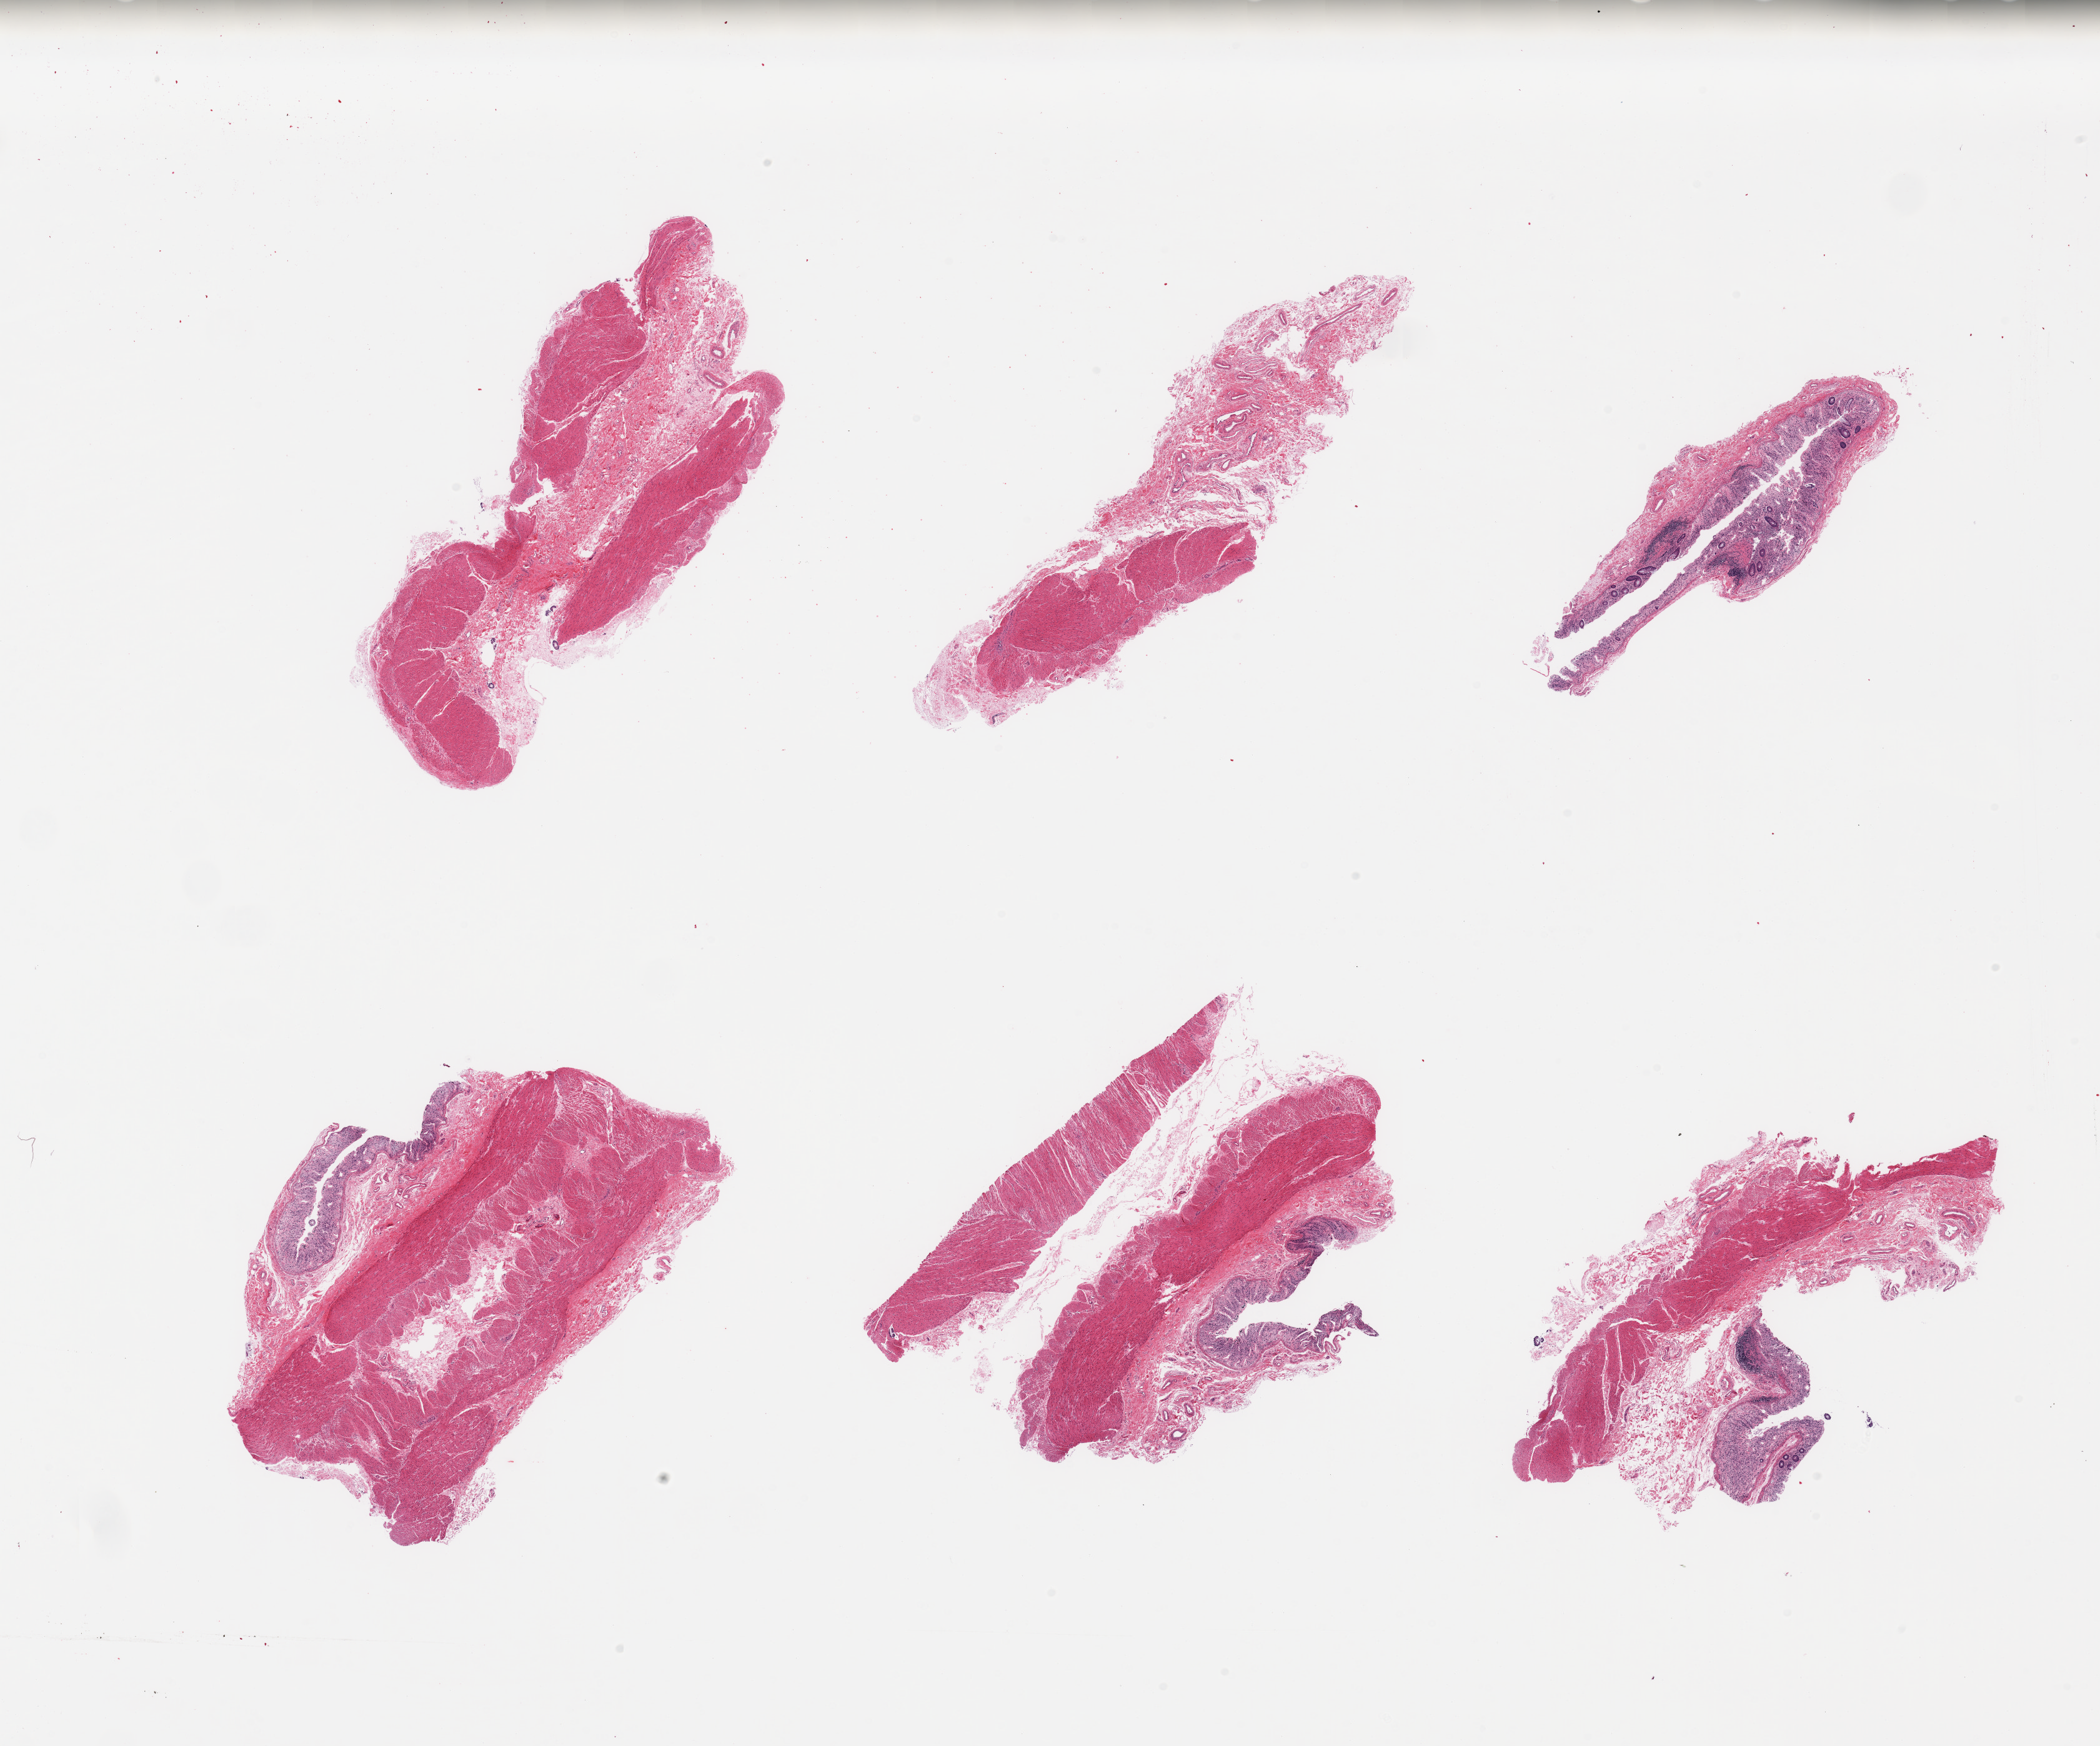
H&E whole-slide image, brightfield, whole scanned area (about 26.6 x 22.1 mm, acquisition: 20x scan) shown as a low-resolution overview. PAXgene-fixed paraffin-embedded (PFPE) section. Section of transverse colon (target tissue). Tissue donor sample.
• pathologist's review note for this sample: 6 pieces, mucosa up to ~0.4mm, glandular mucosa with advanced autolysis/sloughing